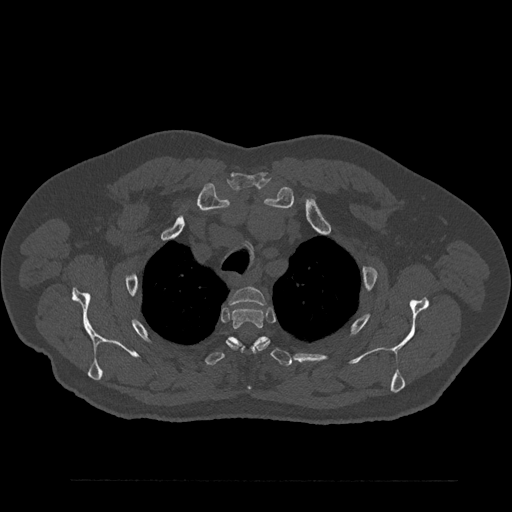
CT including the spine, one axial slice; slice 677 of 797 in the series (ordered by position); reconstruction kernel Br40s/3; bone window (W 1800 / L 400 HU); 0.5 mm slice thickness; 512 × 512 image matrix, field of view 430 × 430 mm. Patient: male, 61 years. From the clinical record (not read from this slice): primary cancer: prostate.
Annotated regions visible in this slice (semi-automatic segmentation, software-assisted and operator-edited):
- T2 vertebra: bounding box <230,287,266,305> (left, top, right, bottom; pixels)
- T3 vertebra: <227,307,269,388>
- T4 vertebra: <205,336,292,366>